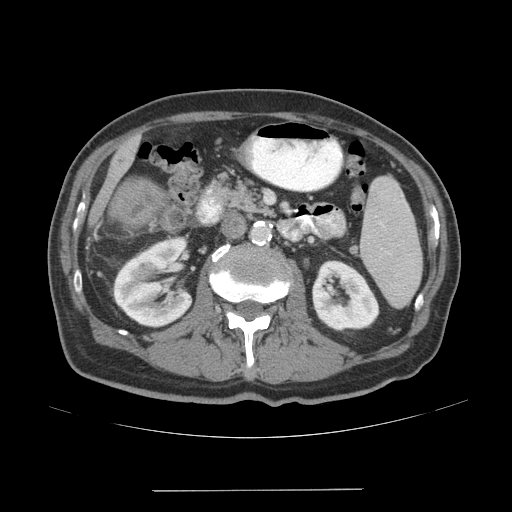
Contrast-enhanced abdominal CT (liver protocol), one axial slice; slice 9 of 77 in the series (ordered by position); reconstruction kernel STANDARD; 140 kVp; soft-tissue window (W 400 / L 40 HU); 2.5 mm slice thickness; 512 × 512 image matrix, field of view 400 × 400 mm. From the clinical record (not read from this slice): diagnosis: hepatocellular carcinoma (patient treated with transarterial chemoembolisation; whether this scan precedes or follows treatment is not stated here); TNM stage (as recorded): Stage-IVA; Child-Pugh class: A.
Annotated regions visible in this slice (semi-automatic segmentation, software-assisted and operator-edited):
- liver parenchyma outside the tumour (the mass and vessels are separate outlines, so this box may not span the whole liver): bounding box <86,137,138,249> (left, top, right, bottom; pixels)
- mass: <111,179,161,223>